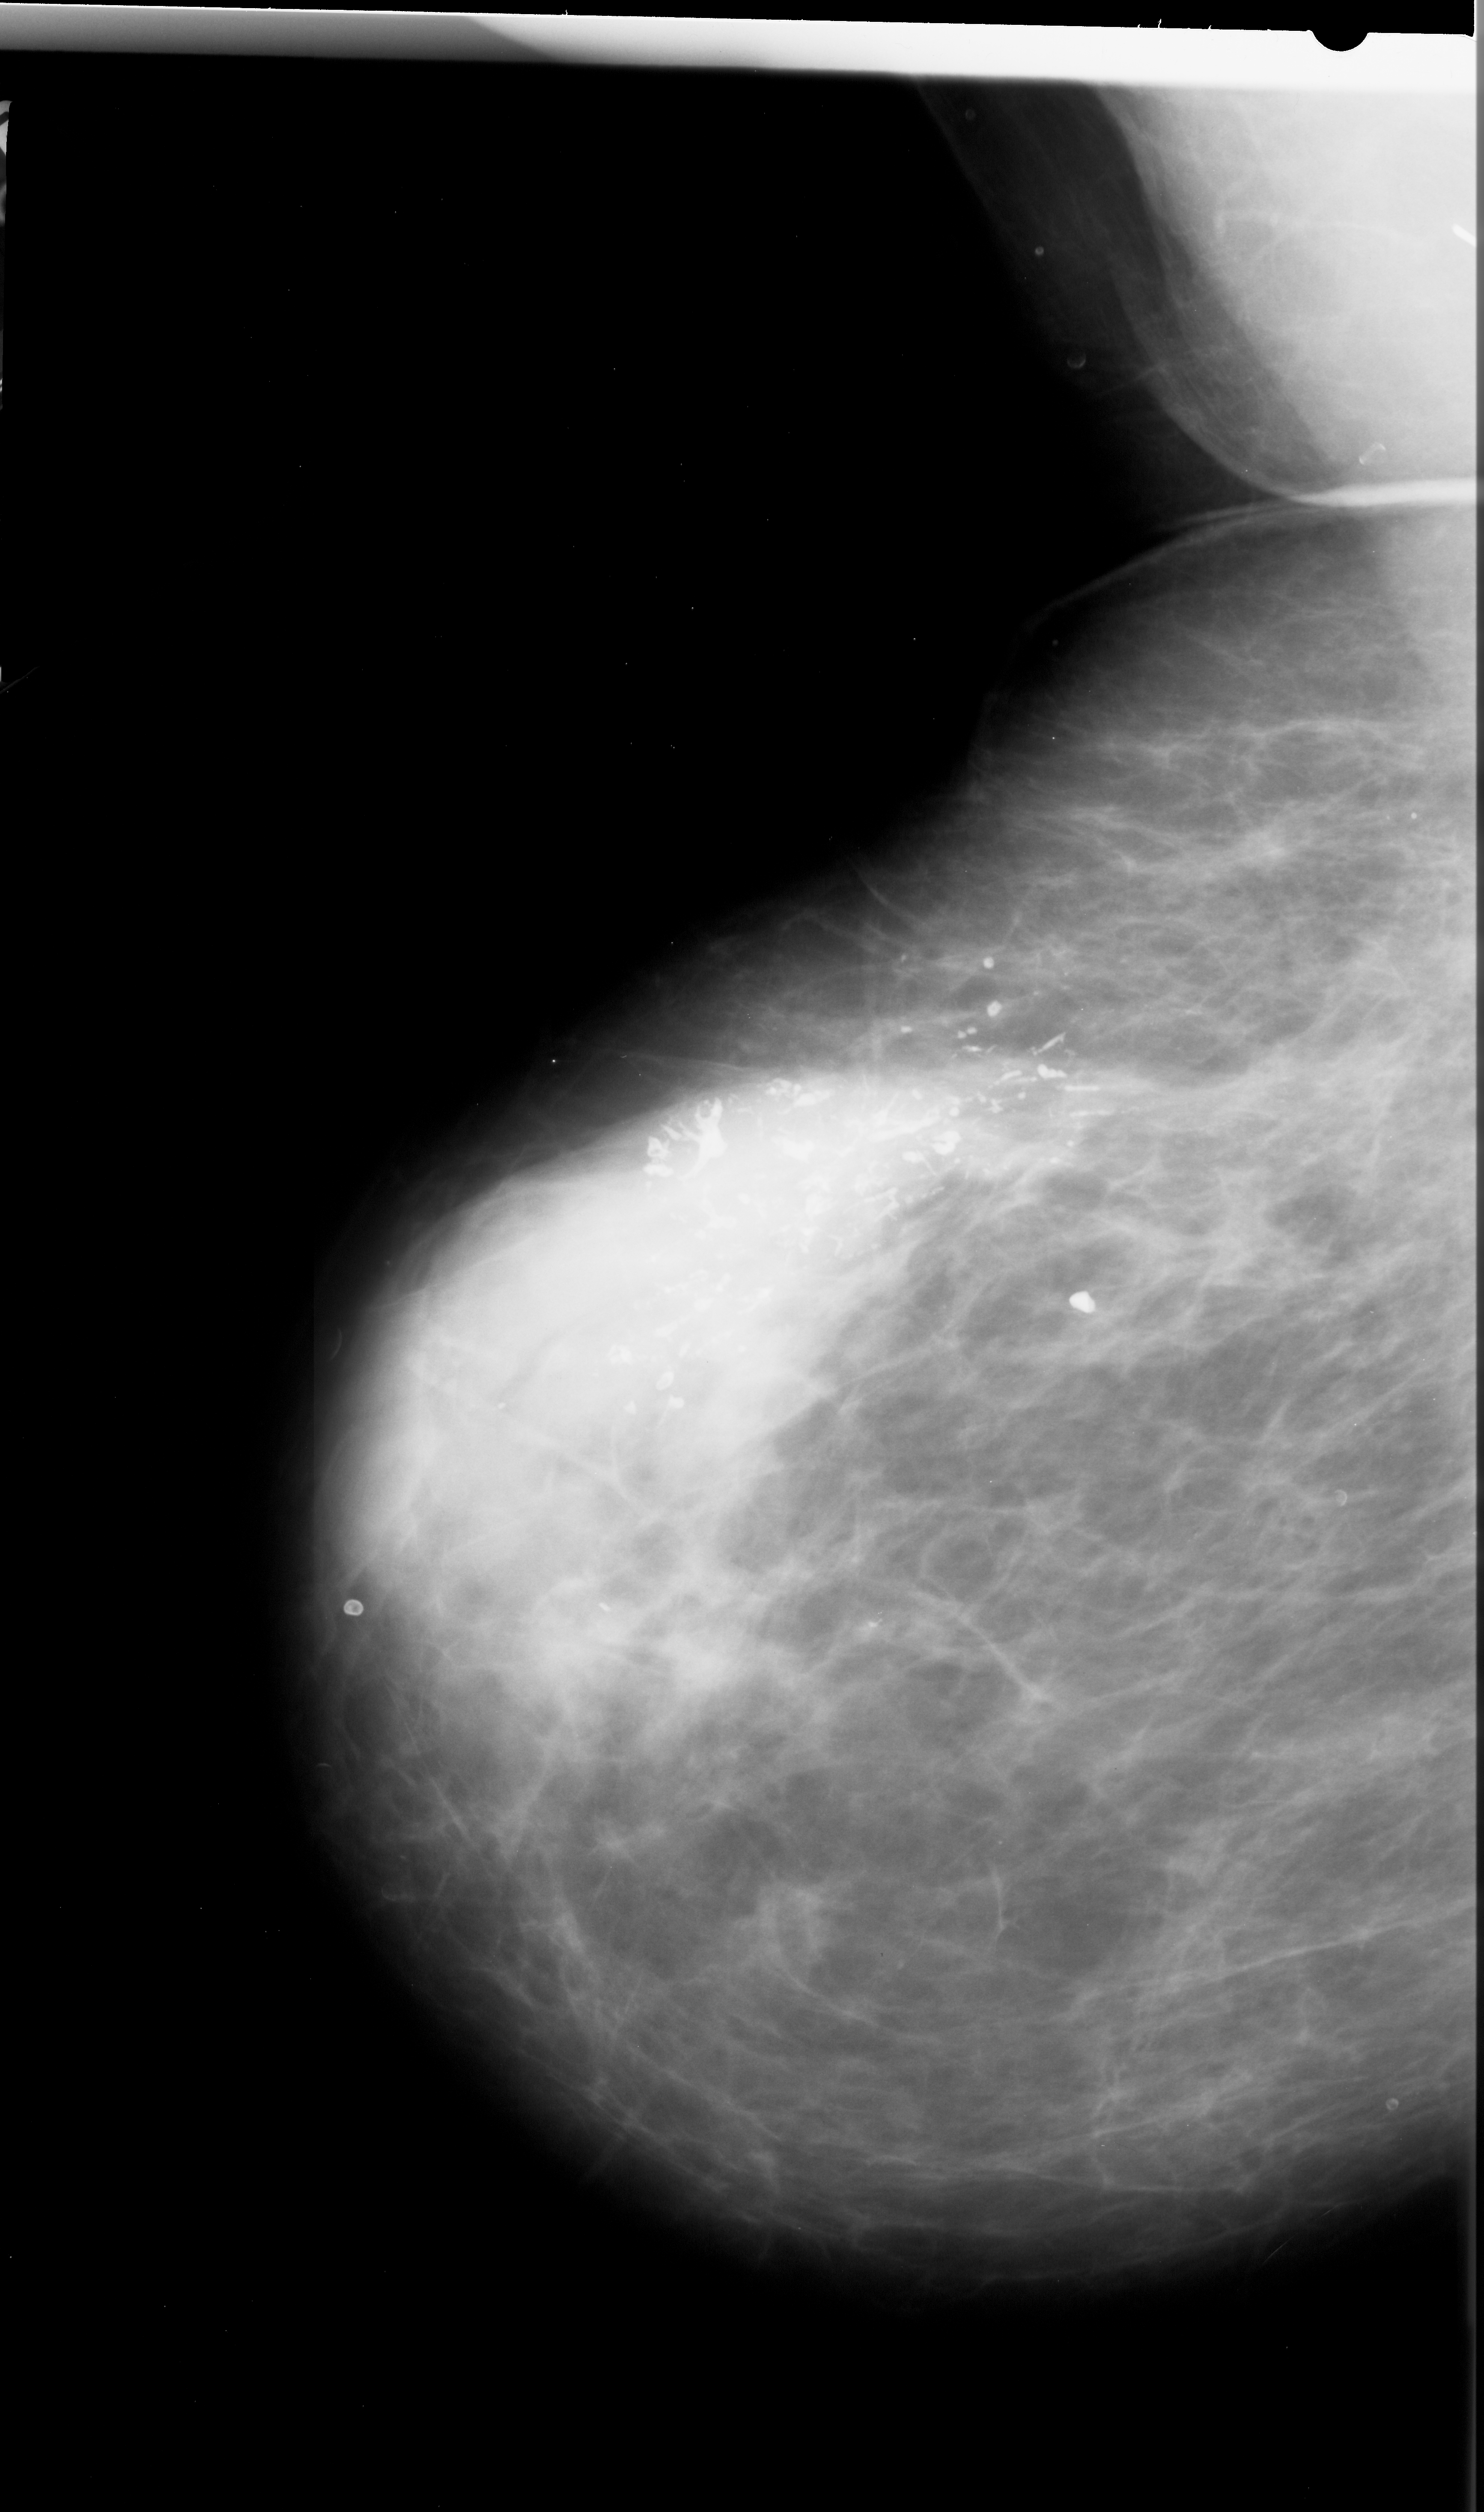
Mammogram (digitized film); left breast; mediolateral oblique (MLO) view; BI-RADS breast density category 4 (scale 1–4); 1484 × 2512 image matrix.
Expert-marked regions of interest on this image (one box per marked abnormality):
- calcifications, morphology pleomorphic, distribution segmental; BI-RADS assessment category 5; subtlety rating 5 on a 1 (subtle) to 5 (obvious) scale; pathology (as recorded): malignant: bounding box <330,893,1297,1477> (left, top, right, bottom; pixels)